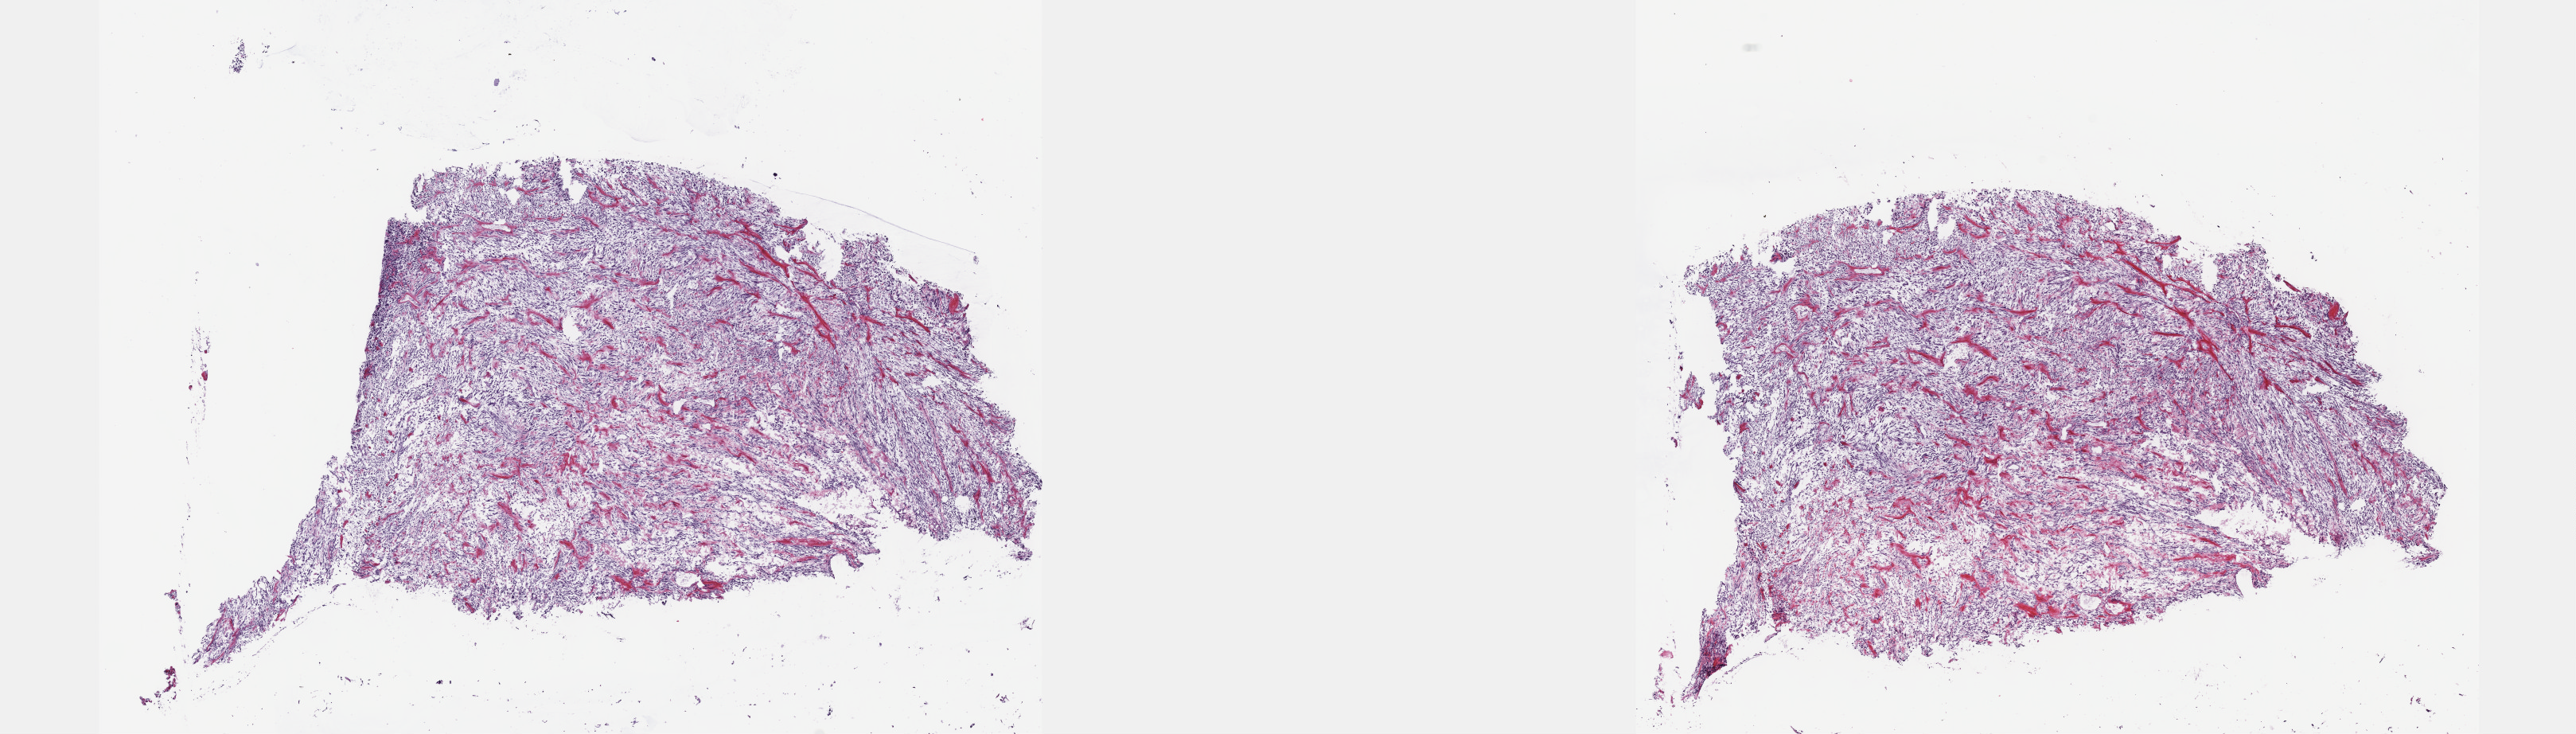
Hematoxylin and eosin (H&E) stained whole-slide image — whole scanned area (about 26.2 x 7.4 mm) shown as a low-resolution overview; frozen section from the top of the tissue portion; sample: primary tumour, corpus uteri. Patient: female, age at initial diagnosis 57 years. Slide review estimates, as recorded: tumour cells 90%, tumour nuclei 90%, normal cells 0%, stromal cells 10%, necrosis 0%. Infiltration values recorded for this section: lymphocyte infiltration 0%, monocyte infiltration 0%, neutrophil infiltration 0%.
Histologic diagnosis: Myxoid leiomyosarcoma (isthmus uteri).